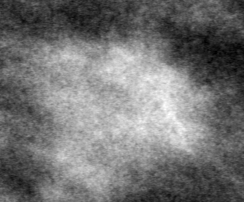
Cropped region of a digitized screen-film mammogram centred on a radiologist-marked abnormality, right breast, MLO view, BI-RADS breast density category 2 (scale 1–4).
Mass, shape irregular, margins ill defined; BI-RADS assessment category 5; subtlety rating 3 on a 1 (subtle) to 5 (obvious) scale; pathology (as recorded): malignant.